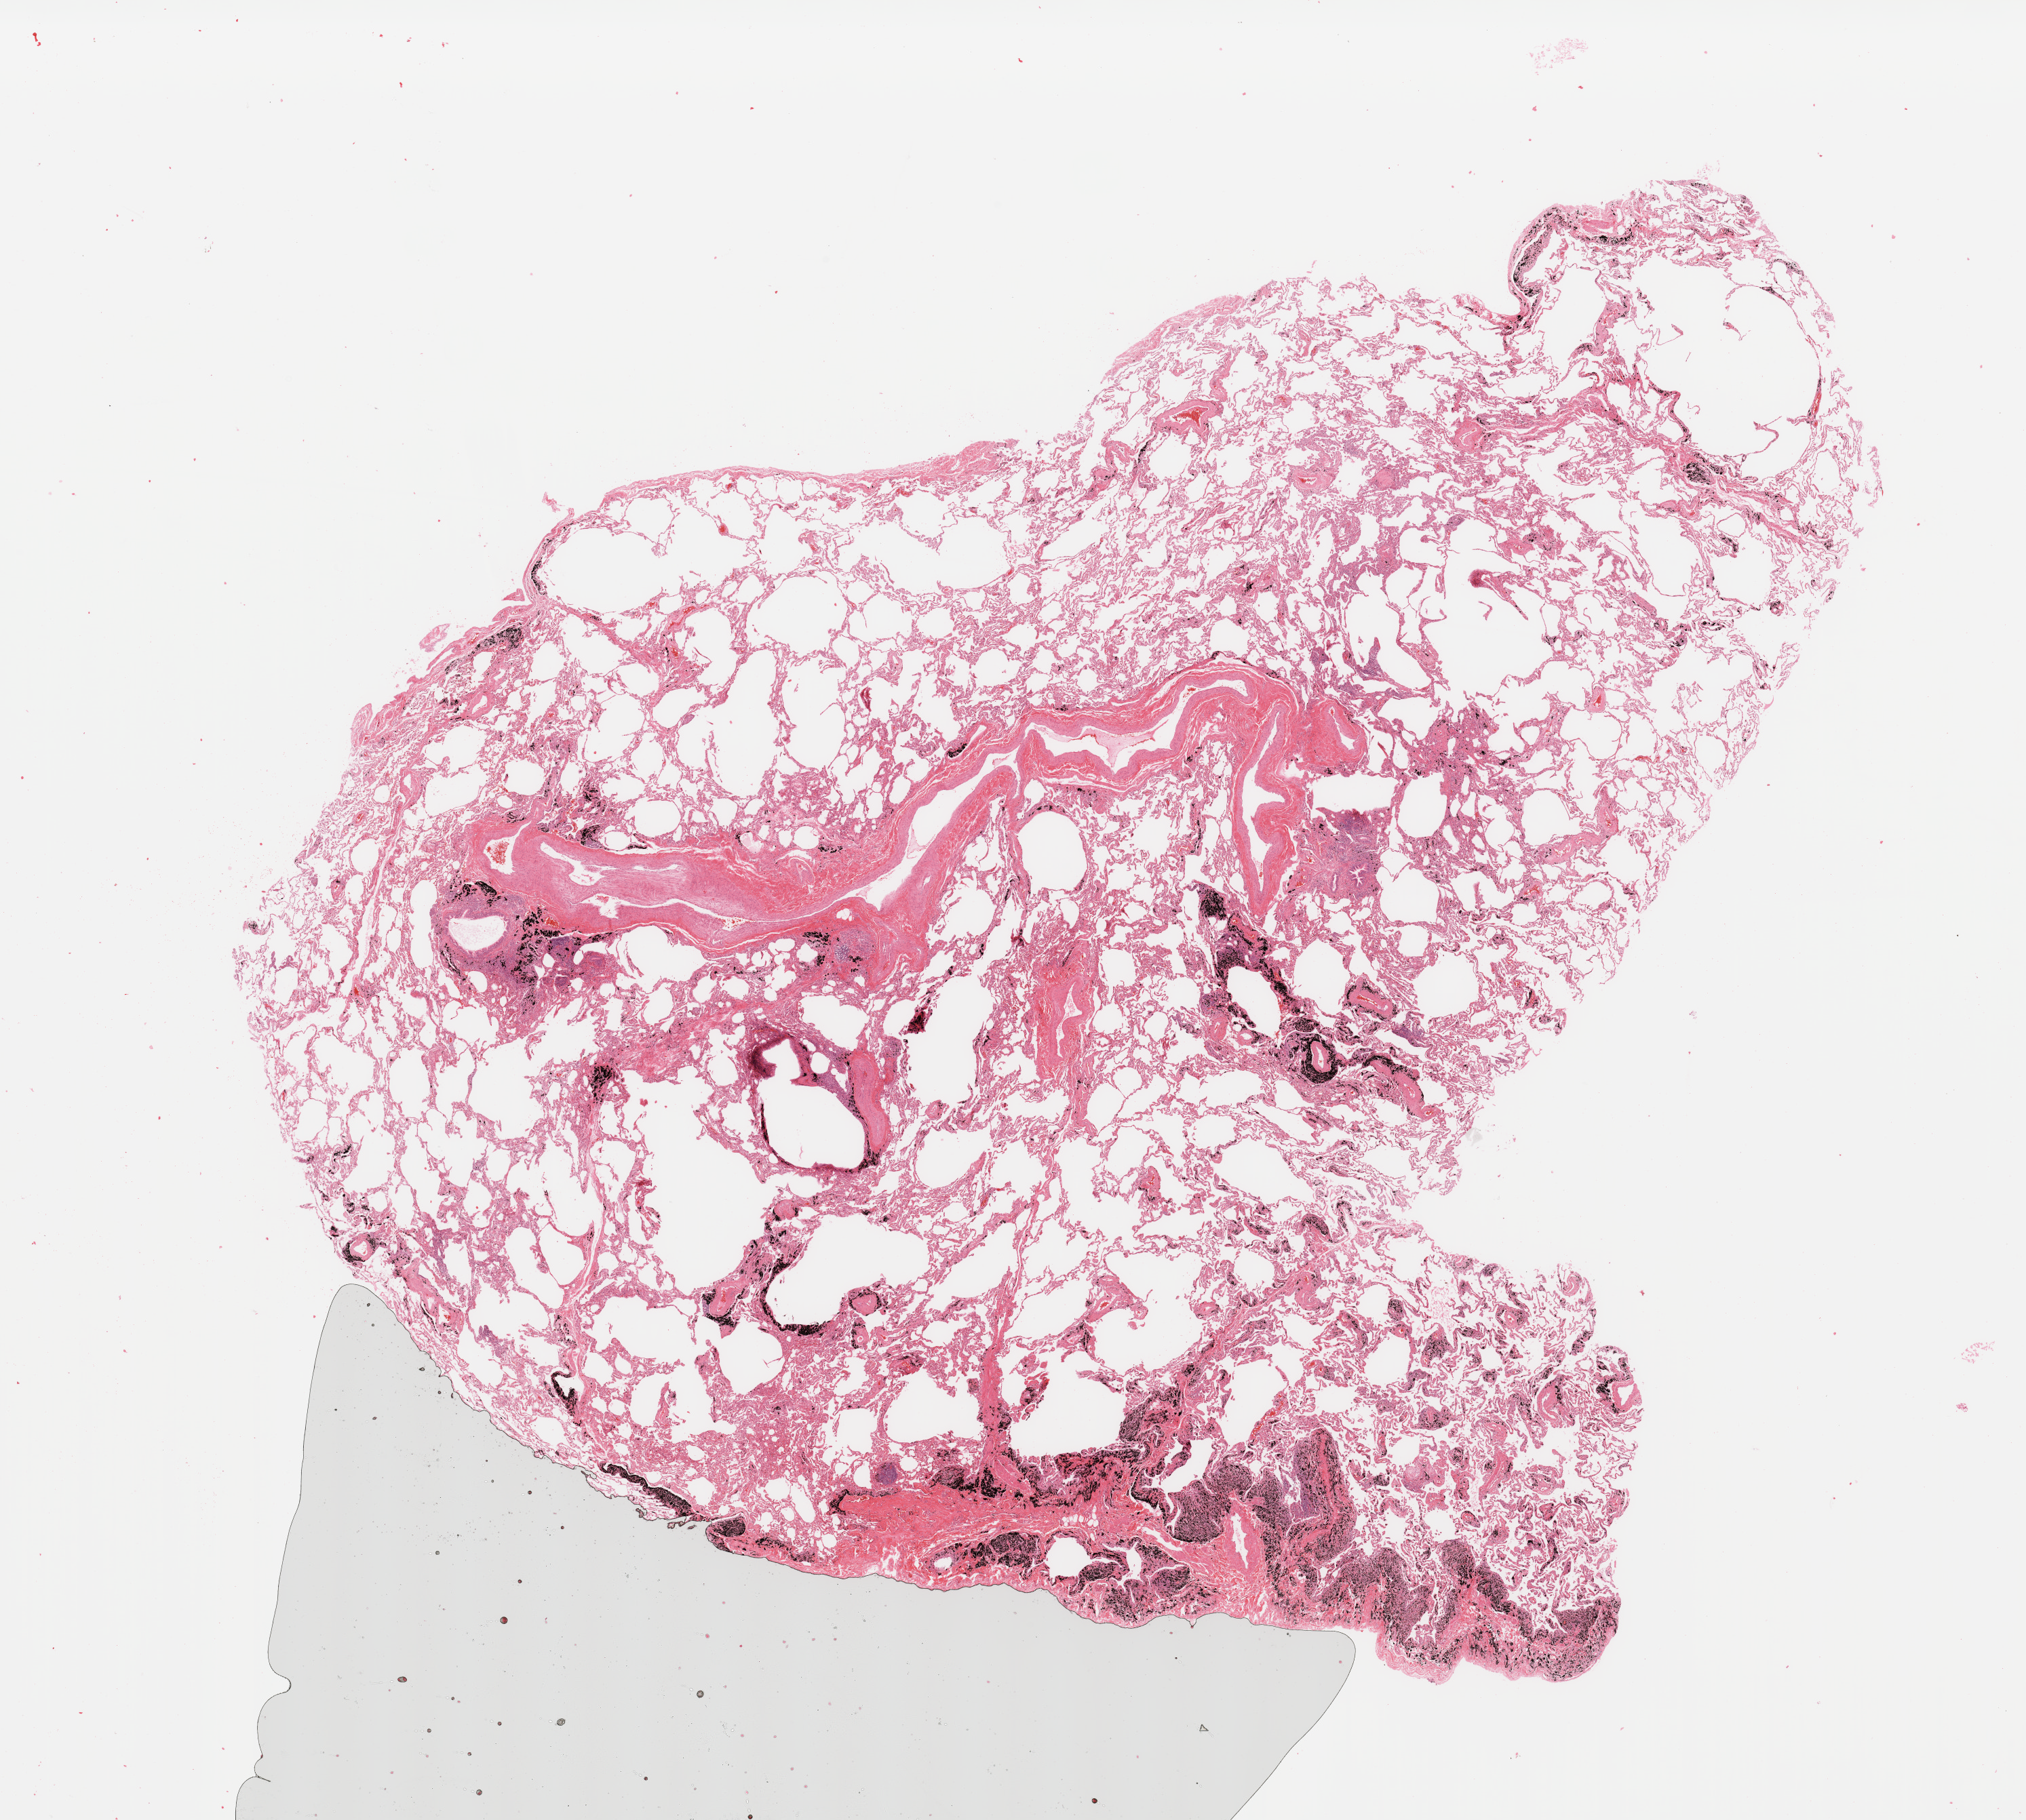
Digitized H&E tissue section (whole slide) — low-resolution overview of the scanned area, about 23.6 x 21.2 mm, normal (non-tumour) tissue sample, lung. Male, 72 y/o.
This section: normal (non-tumour) tissue from the same patient. Patient diagnosis: Squamous cell carcinoma, NOS.